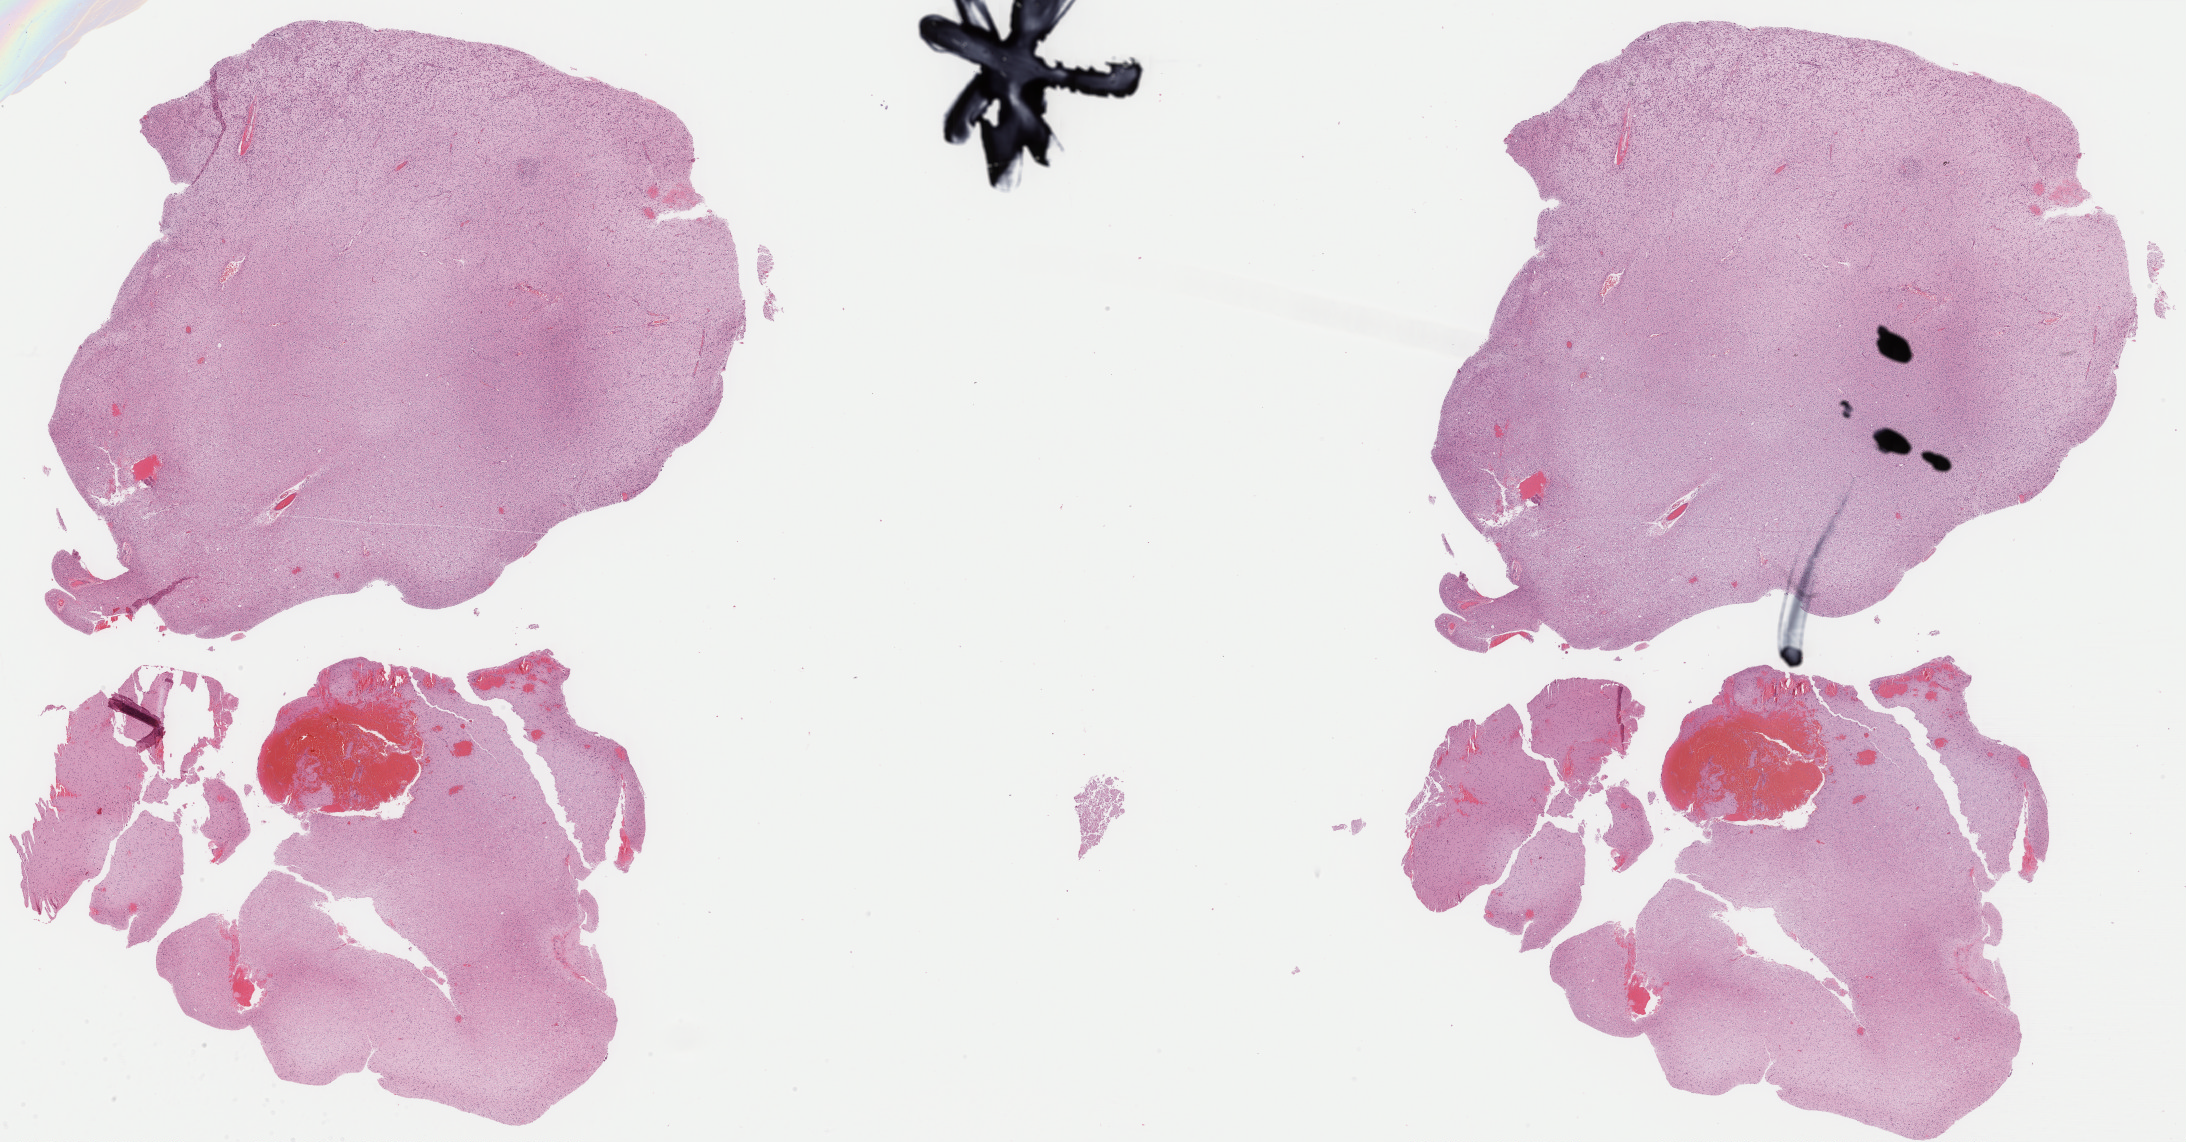
H&E-stained whole-slide image, a low-resolution overview of the entire scanned area, about 34.5 x 18.0 mm (slide scanned at 40x); formalin-fixed paraffin-embedded (FFPE) diagnostic section; sample: primary tumour, brain. Female, age 27 years at initial diagnosis. Histologic grade: G3 (poorly differentiated).
Laterality: left. Diagnosis: Mixed glioma (temporal lobe).